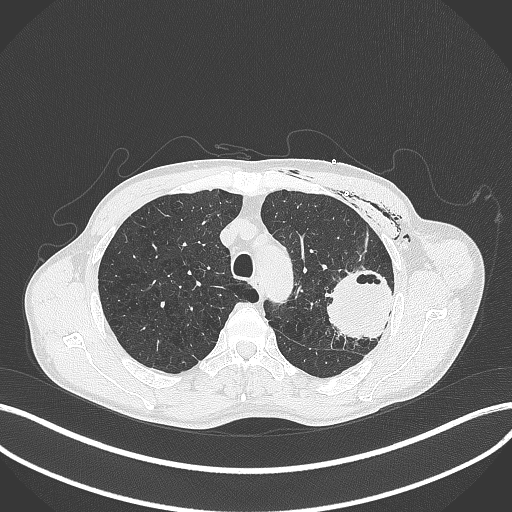
Chest CT, one axial slice; slice 309 of 457 in the series (ordered by position); lung window (W 1500 / L -600 HU); 1 mm slice thickness; 512 × 512 image matrix, field of view 400 × 400 mm. Male patient, age 58 years. From the clinical record (not read from this slice): clinical TNM (as recorded): T3 N0 M0.
Outlined on this slice (bounding box drawn by a radiologist):
- lung tumour (recorded histology: adenocarcinoma): bounding box [x1, y1, x2, y2] px = [327, 262, 394, 344]